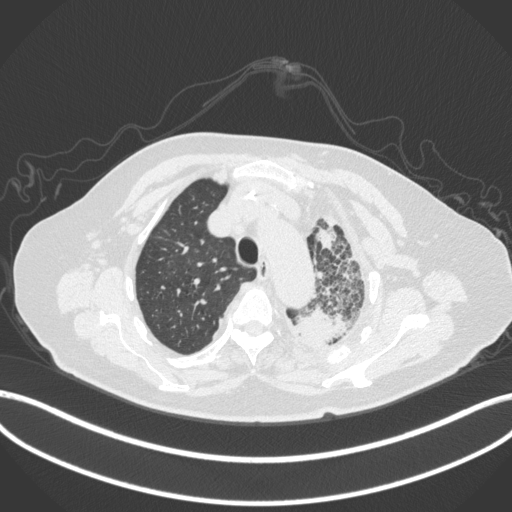
Chest CT, one axial slice. 120 kVp. Lung window (W 1500 / L -600 HU). 1 mm slice thickness. 512 × 512 image matrix, field of view 400 × 400 mm. Female patient, age 75 years. From the clinical record (not read from this slice): clinical TNM (as recorded): T3 N3 M1.
Outlined on this slice (rectangle marked by the reading radiologist):
- lung tumour (recorded histology: adenocarcinoma): bounding box [x1, y1, x2, y2] px = [289, 301, 352, 355]